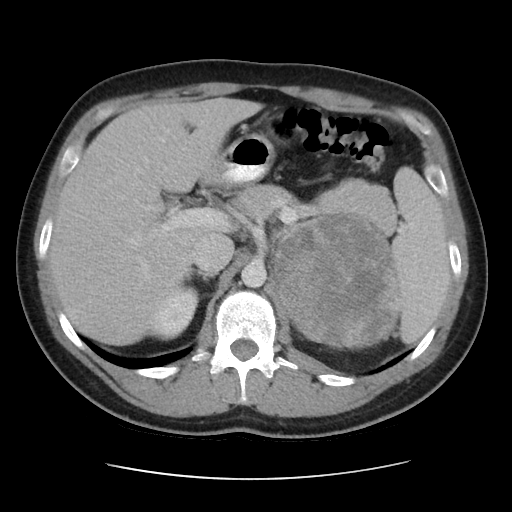
Contrast-enhanced abdominal CT, one axial slice; slice 29 of 48 in the series (ordered by position); 120 kVp; intravenous contrast given; soft-tissue window (W 400 / L 40 HU); 5 mm slice thickness; 512 × 512 image matrix. Male patient, age 32 years. Case-level facts recorded for this patient, not image findings: diagnosis: adrenocortical carcinoma; tumour side: left adrenal.
Structures marked on this image (semi-automatic segmentation, software-assisted and operator-edited):
- mass: bounding box [x1, y1, x2, y2] px = [275, 217, 396, 347]